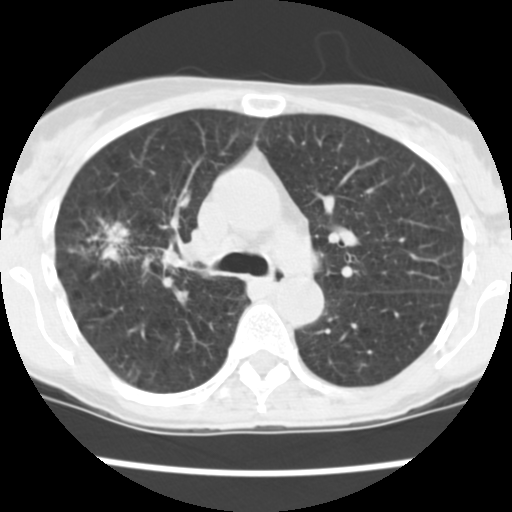
Low-dose screening chest CT, one axial slice; position 161 of 252 along the scan axis; reconstruction kernel STANDARD; lung window (W 1500 / L -600 HU); 2.5 mm slice thickness; 512 × 512 image matrix.
Outlined on this slice (manually delineated by an expert):
- lesion 2 (tumor, lower lobe of right lung): bounding box (x1, y1, x2, y2) in pixels: (100, 220, 129, 262)